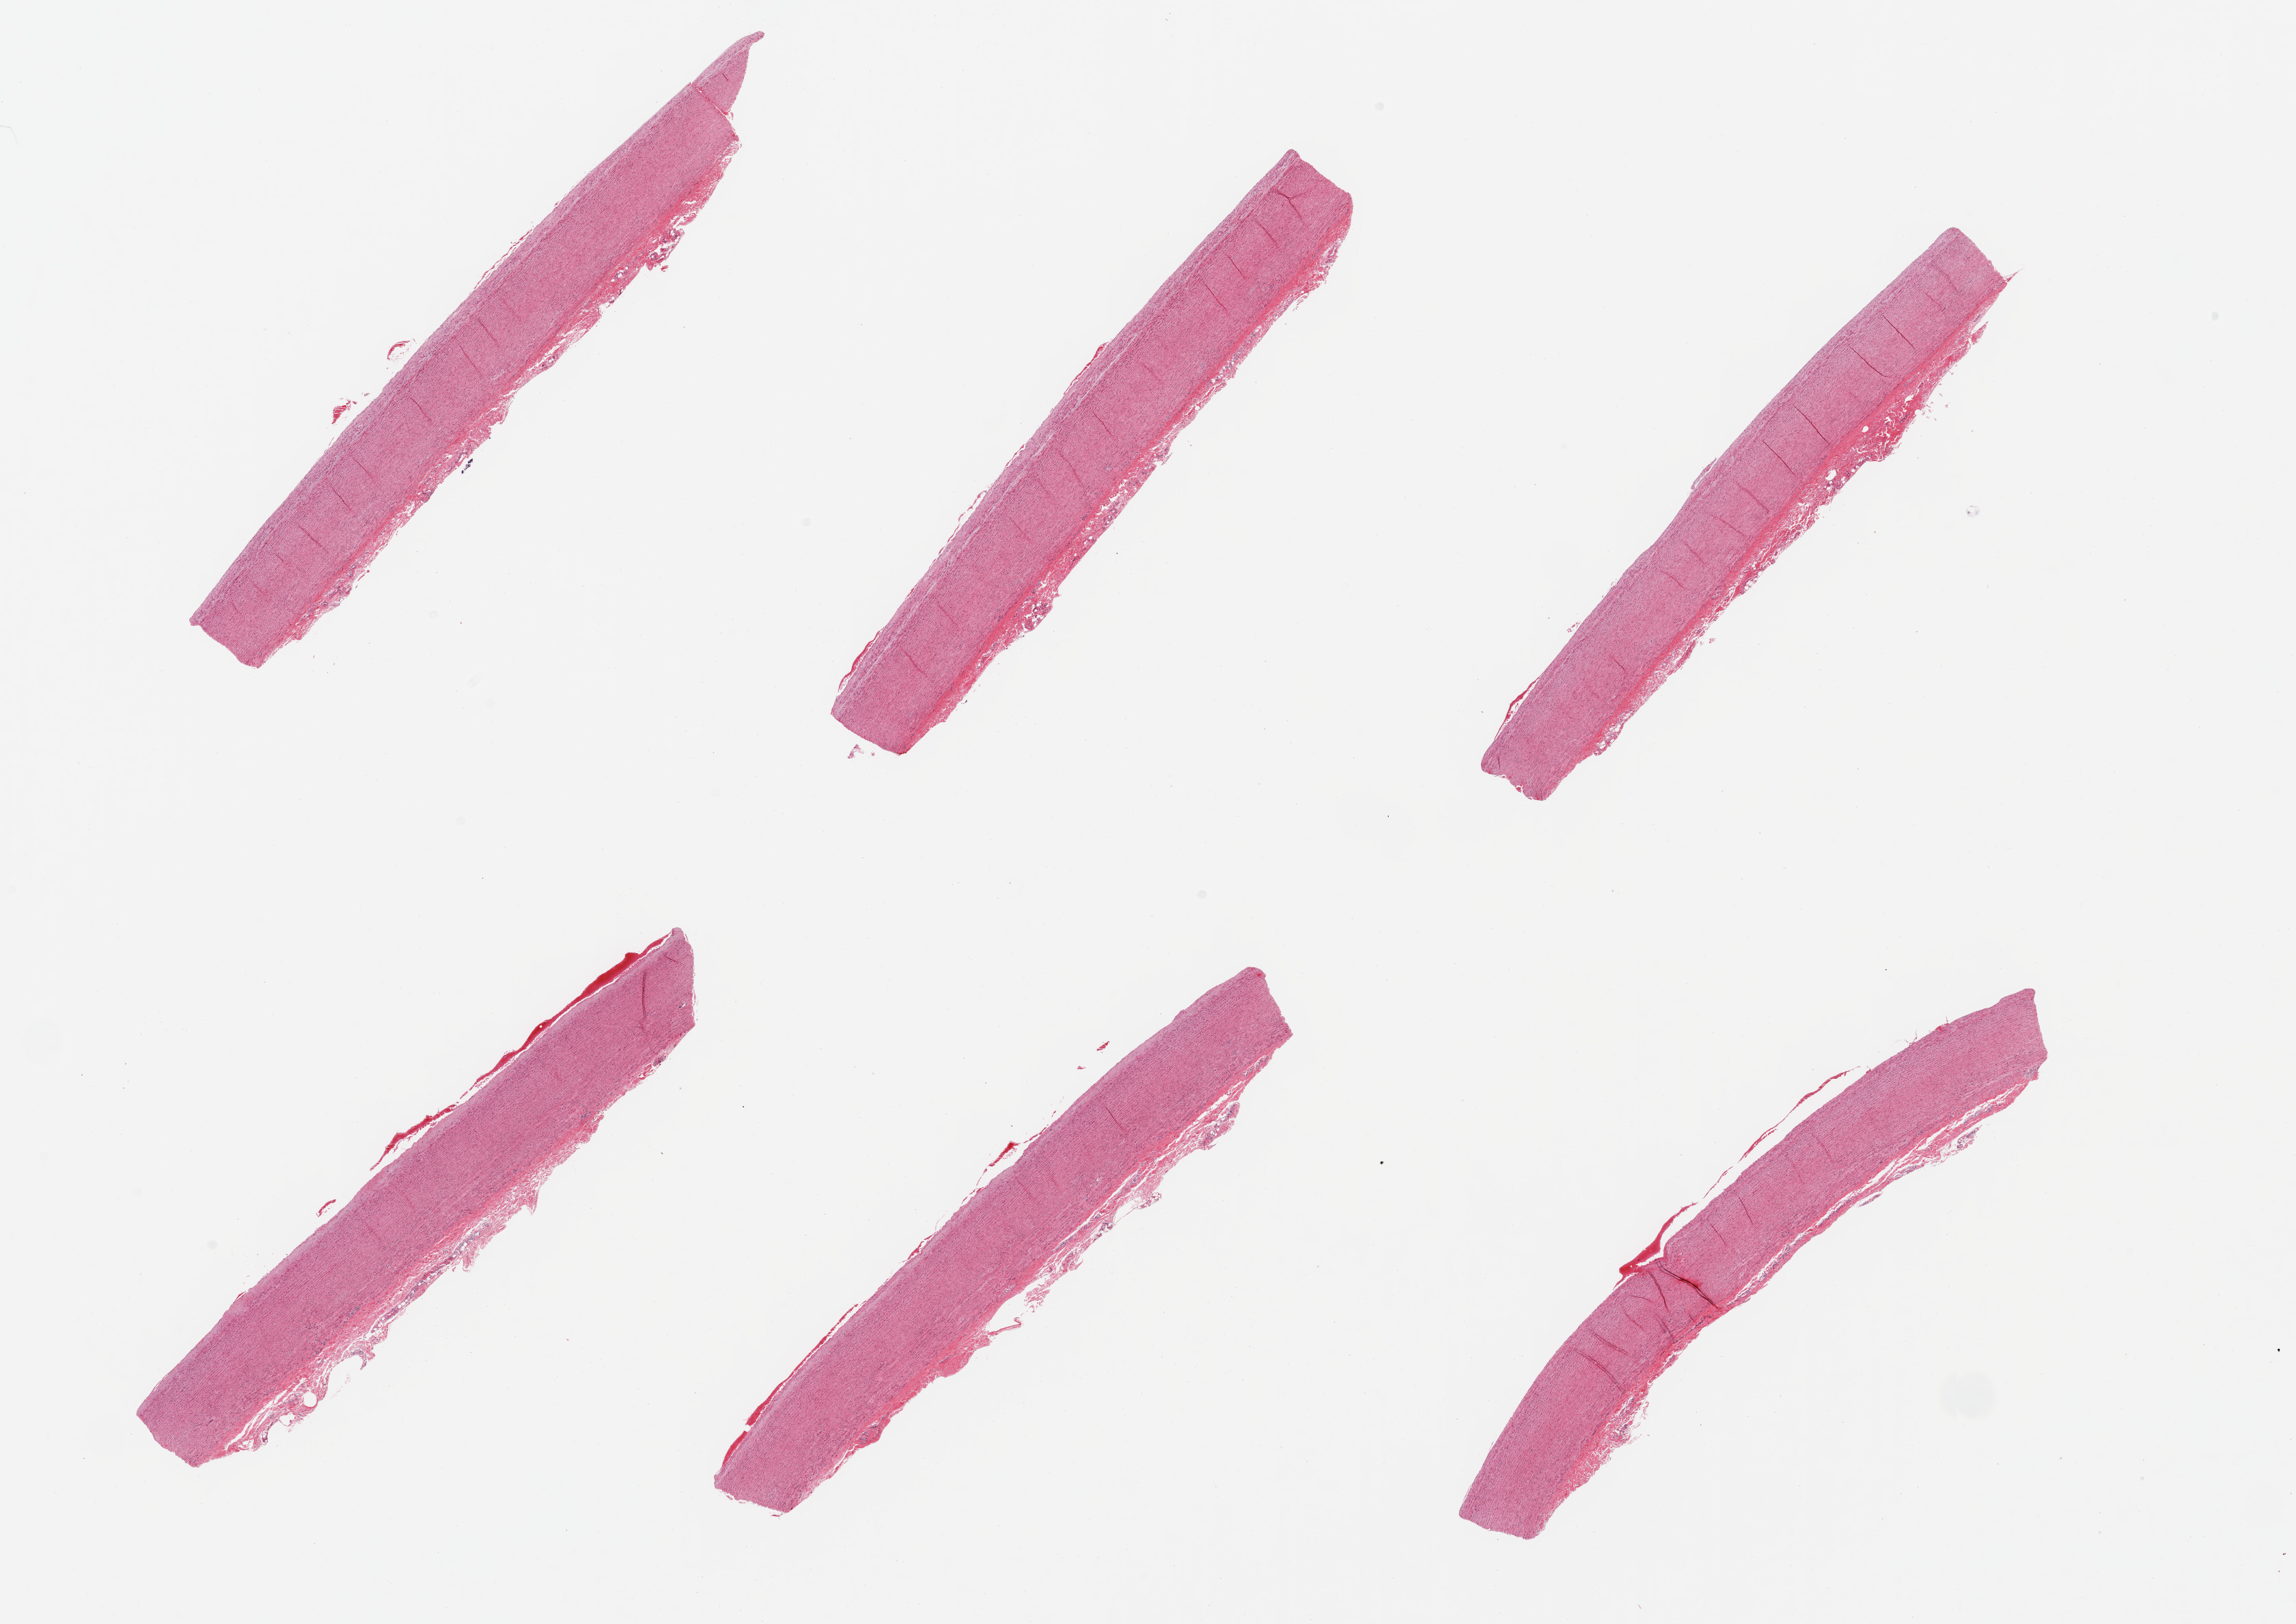
Whole-slide image, haematoxylin and eosin stain, whole scanned area (about 26.6 x 18.8 mm) shown as a low-resolution overview. PAXgene-fixed, paraffin-embedded tissue. Sampled site (target tissue): aorta. Donor tissue sample. Donor: female.
• review note (as recorded): 6 pieces; no plaques; well trimmed